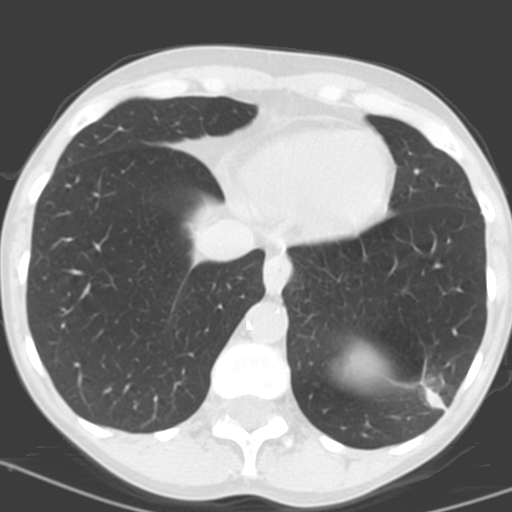
Low-dose screening chest CT, axial slice; baseline annual screen; lung window (W 1500 / L -600 HU); standard (soft-tissue) reconstruction kernel (C). Female participant, aged 56 years at enrolment. Current smoker at enrolment.
Lesion marked by an expert reader, bounding box [x1, y1, x2, y2] px = [395, 354, 470, 422]. The exam's reader record, not a measurement of the box and not confirmed to be the same lesion: non-calcified nodule or mass ≥4 mm, left lower lobe, 31 × 23 mm, poorly defined margins, soft tissue attenuation, pre-existing on the prior screen: no. Official screen result: positive, change unspecified: nodule(s) >= 4 mm or enlarging nodule(s), mass(es), or other non-specific abnormalities suspicious for lung cancer. Participant outcome: lung cancer diagnosed 27 days after this screen — squamous cell carcinoma, NOS, left lower lobe, poorly differentiated (G3), stage IB (AJCC 6th edition), 35 mm at pathology.